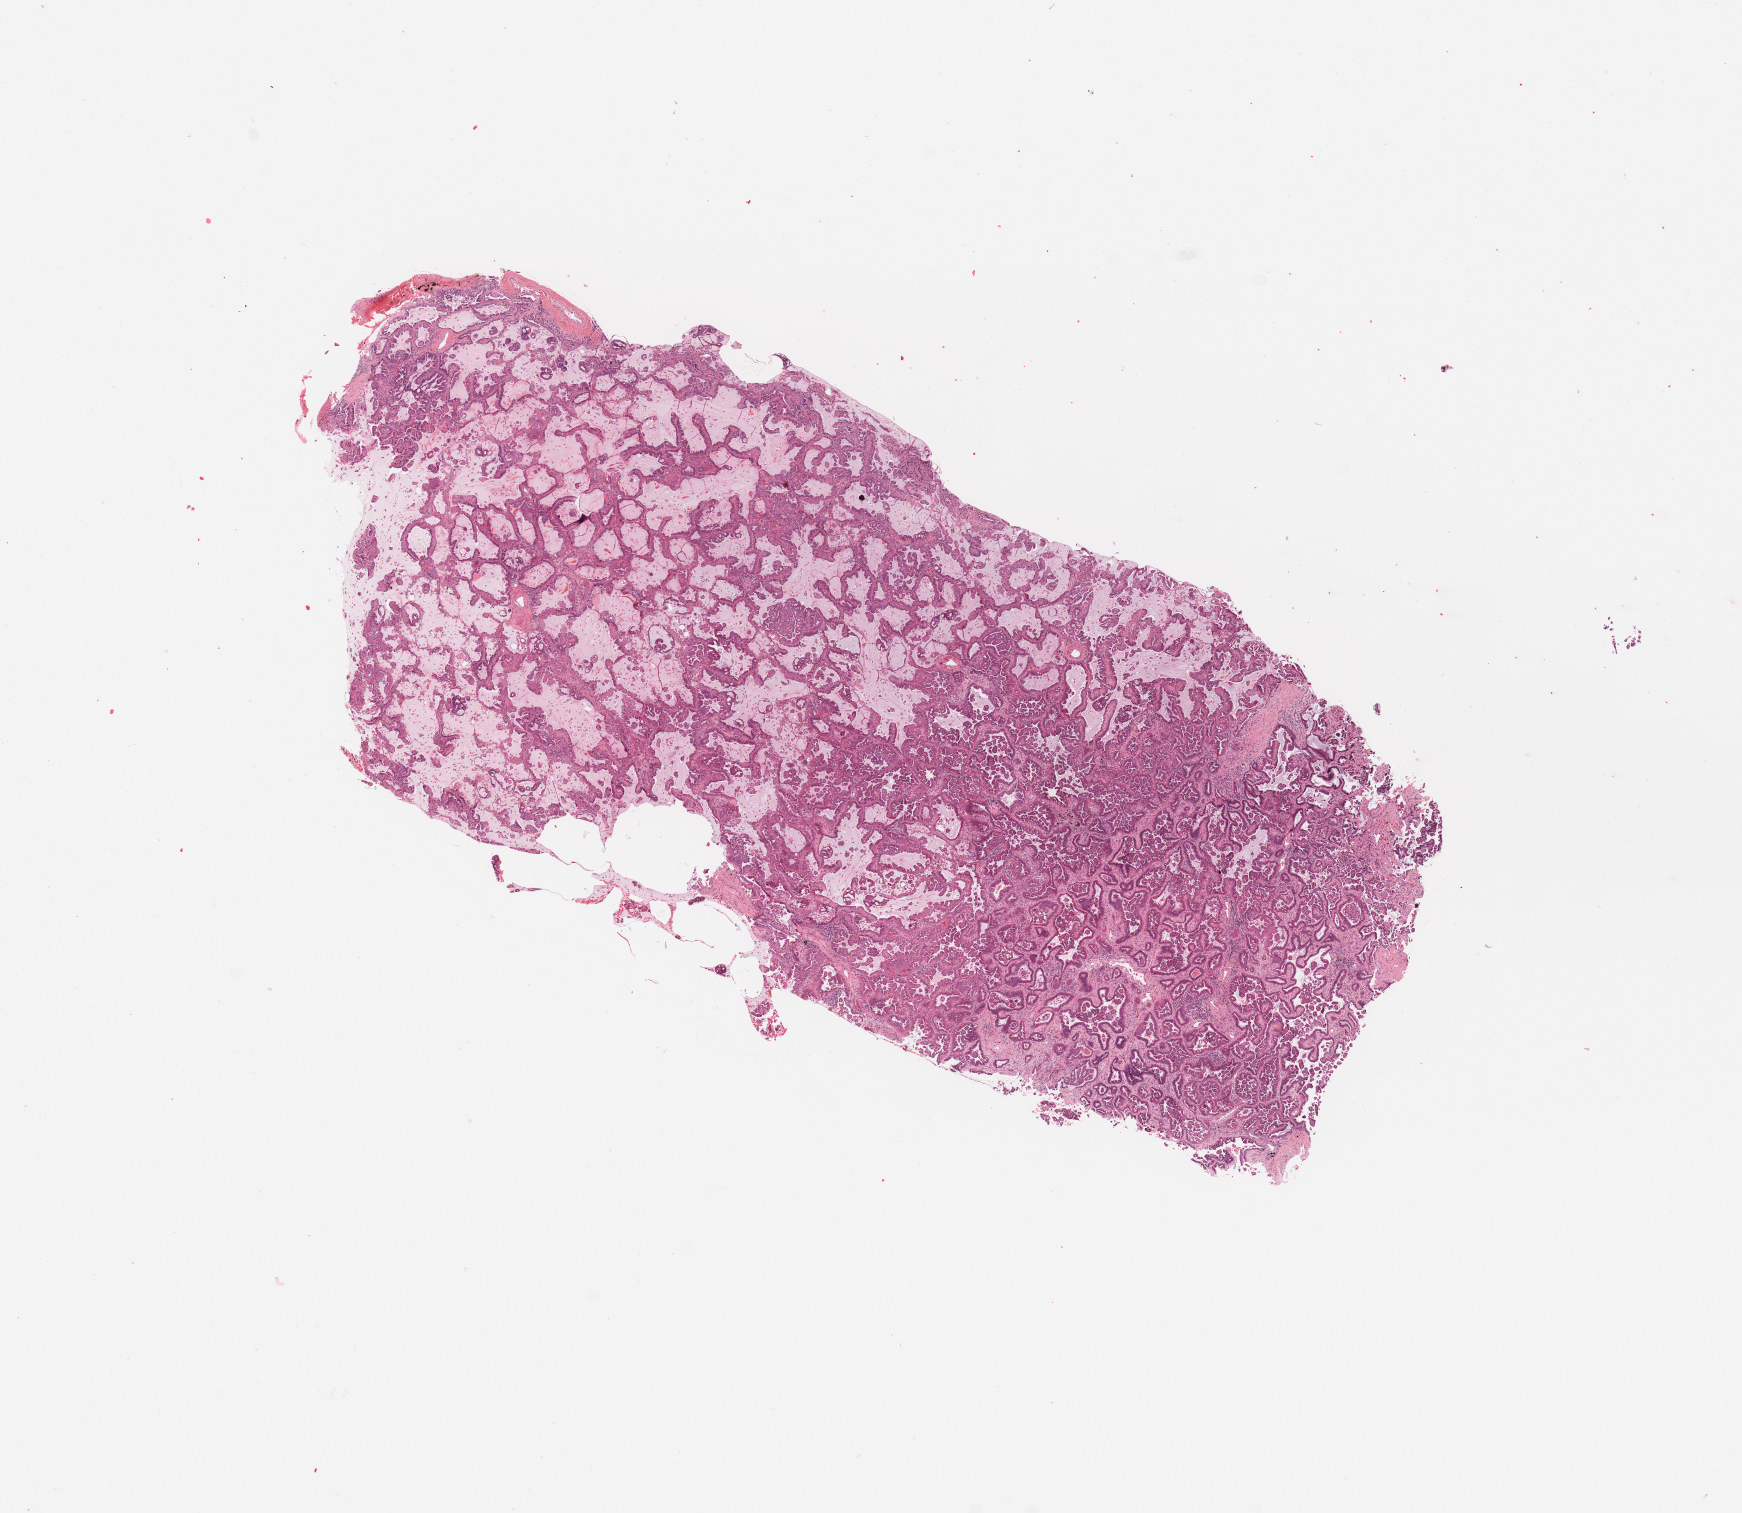
H&E whole-slide image, shown as a low-resolution overview of the whole scanned area (about 13.8 x 12.0 mm, acquisition: 20x scan); tumour tissue sample, sampled site: lung. Patient: male, age 73 years. Histologic grade: G2 (moderately differentiated). Slide review estimates, as recorded: tumour nuclei 70%, necrosis 0%.
AJCC pathologic stage: IIA. Histologic diagnosis: Adenocarcinoma, NOS. Primary tumour site (as recorded): right upper lobe.